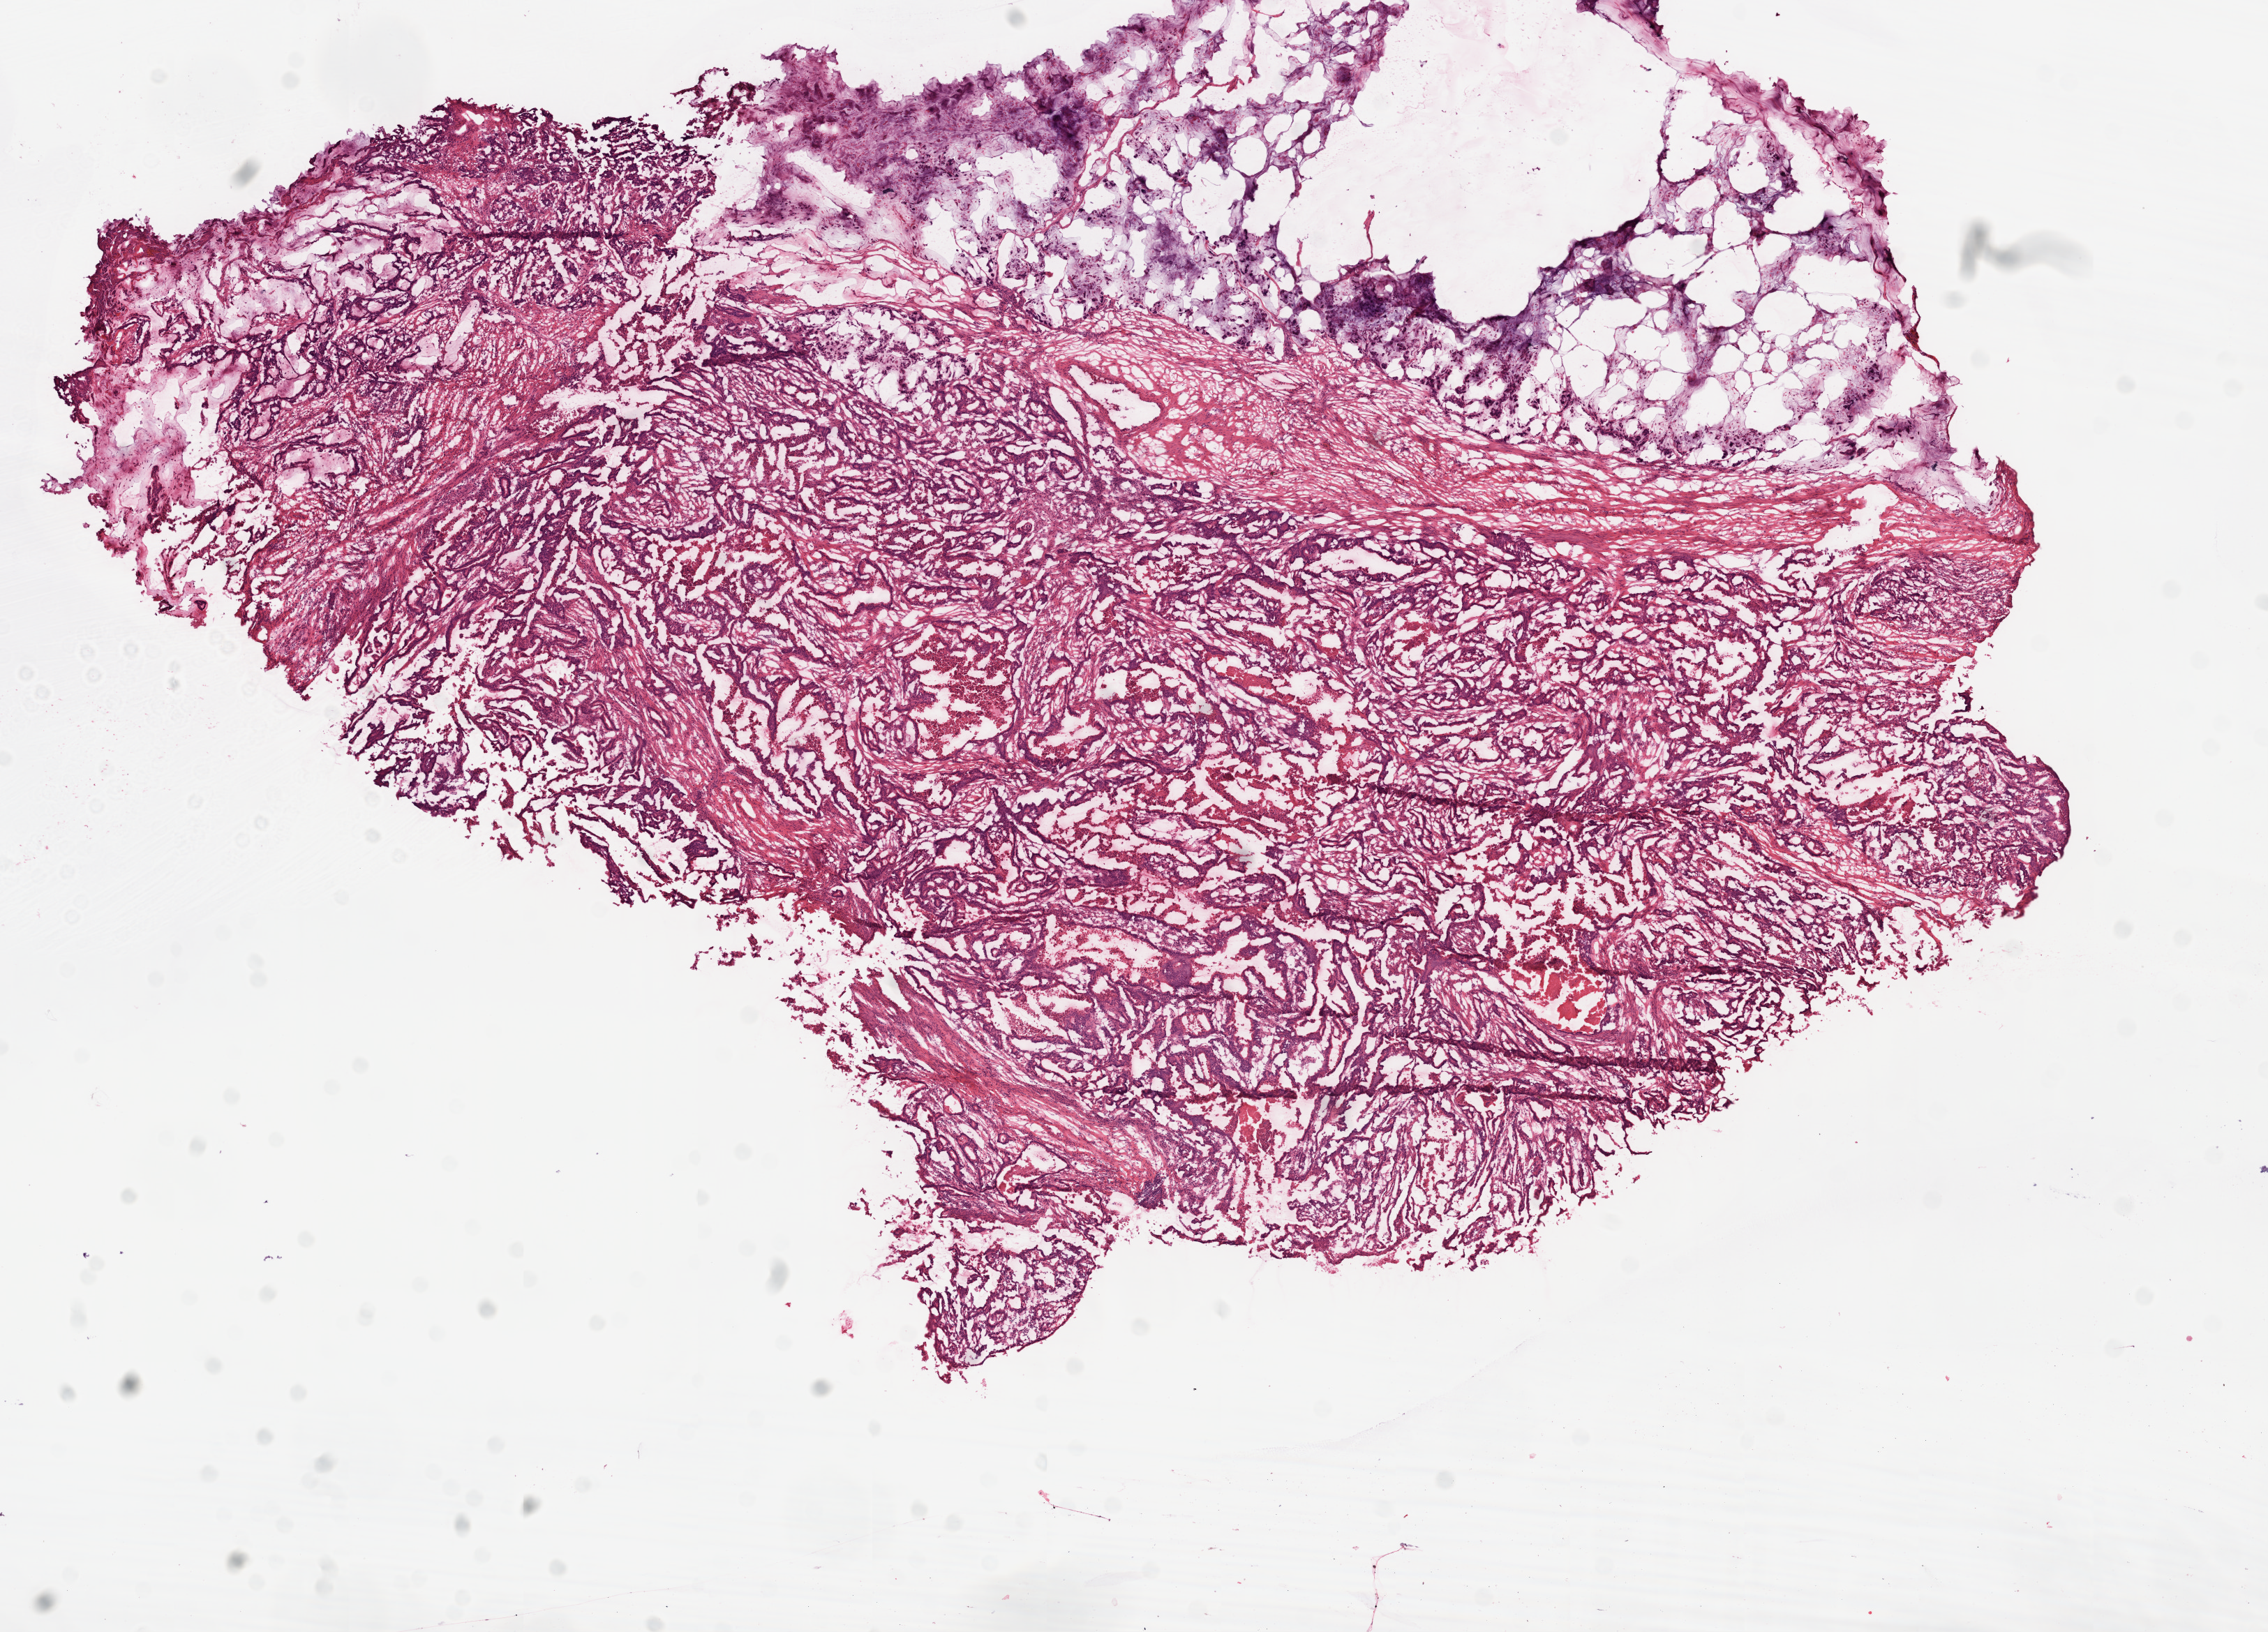
Digitized Hematoxylin and eosin (H&E) stained tissue section (whole slide) — whole scanned area (about 13.0 x 9.4 mm, acquisition: 20x scan) shown as a low-resolution overview; frozen section from the top of the tissue portion; colon, primary tumour sample. Patient: male, age at initial diagnosis 84 years.
Histologic diagnosis: Adenocarcinoma, NOS (cecum).